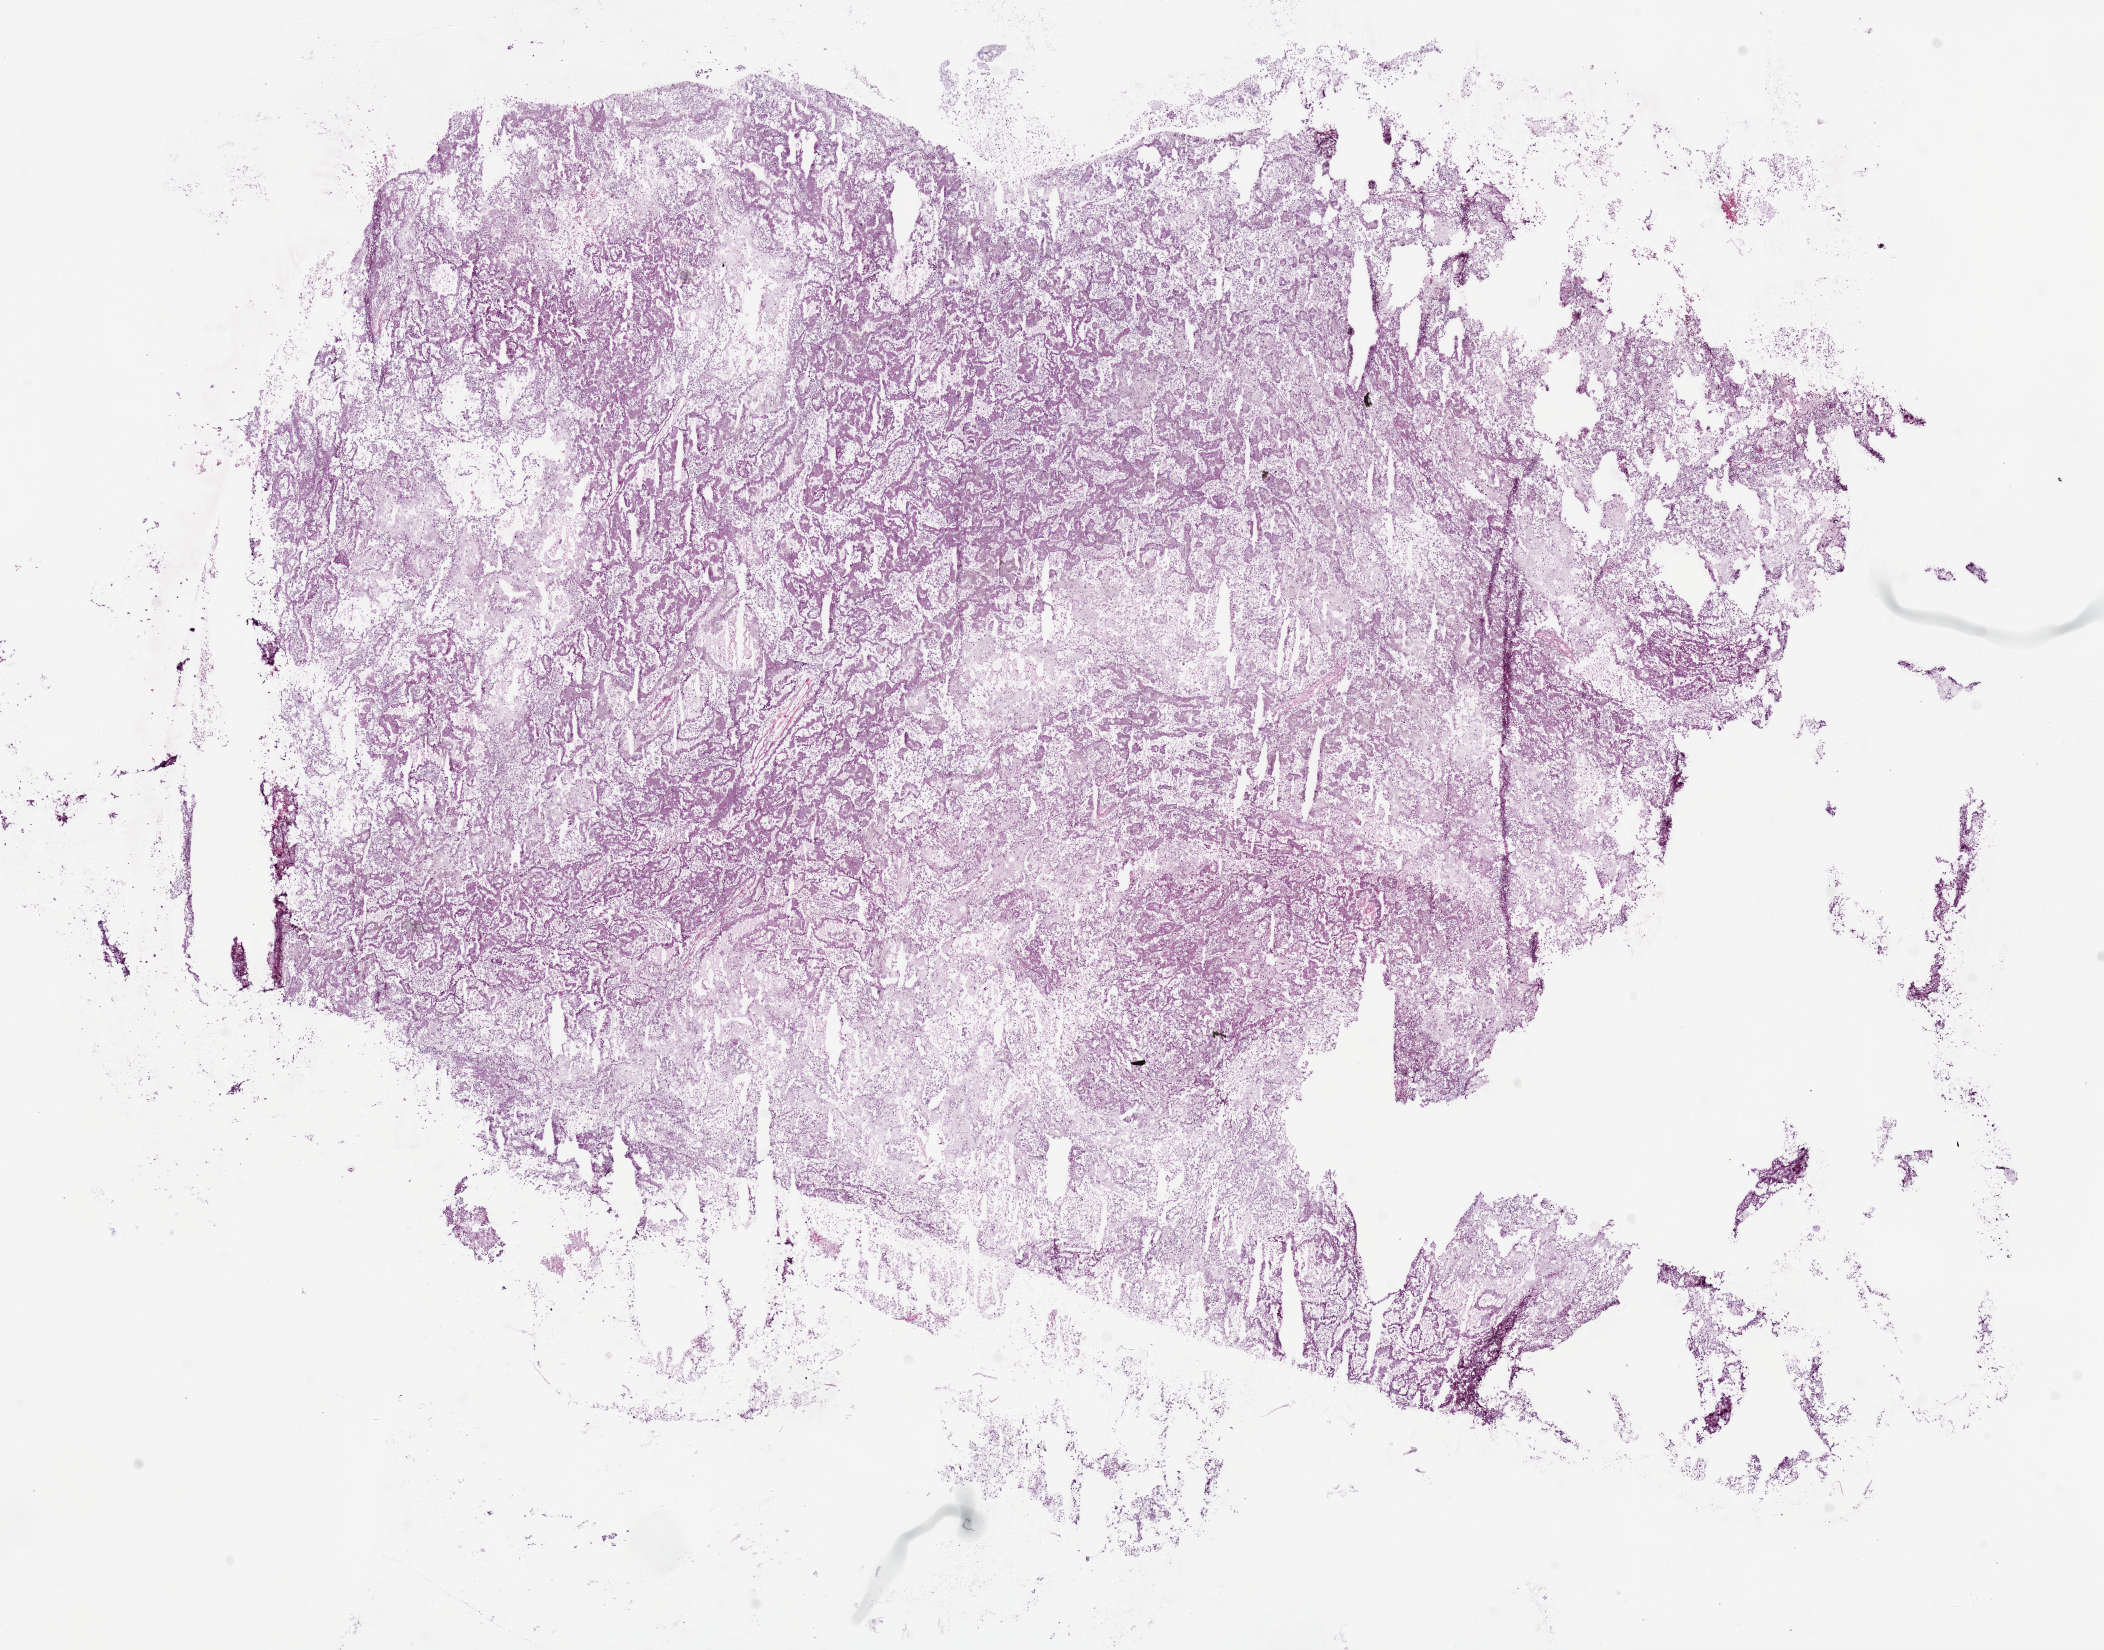
Hematoxylin and eosin (H&E) stained whole-slide image, shown as a low-resolution overview of the whole scanned area (about 16.9 x 13.2 mm), frozen section, sample: primary tumour, kidney. Male, age 73 years at initial diagnosis. Composition of this section per pathologist review: tumour cells 95%, tumour nuclei 50%, normal cells 0%, stromal cells 5%, necrosis 0%.
* AJCC pathologic stage: III (7th edition)
* pathologic diagnosis: Papillary adenocarcinoma, NOS